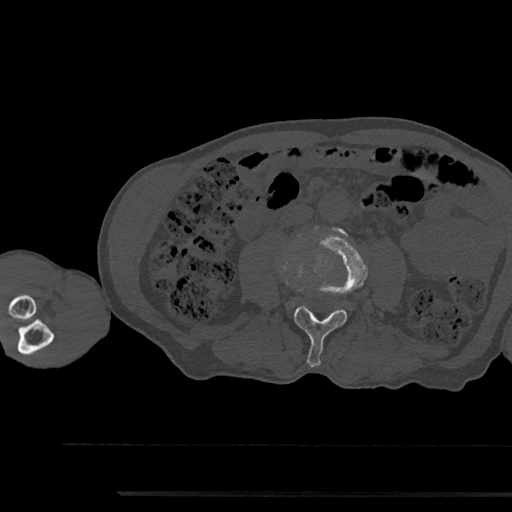
CT including the spine, one axial slice. Position 463 of 797 along the scan axis. Reconstruction kernel Br40s/3. 120 kVp. Bone window (W 1800 / L 400 HU). 512 × 512 image matrix, field of view 367 × 367 mm. Male patient, age 79 years. Case-level facts recorded for this patient, not image findings: primary cancer: prostate.
Annotated regions visible in this slice (semi-automatically segmented with operator editing):
- L3 vertebra: bounding box [x1, y1, x2, y2] px = [294, 228, 367, 367]